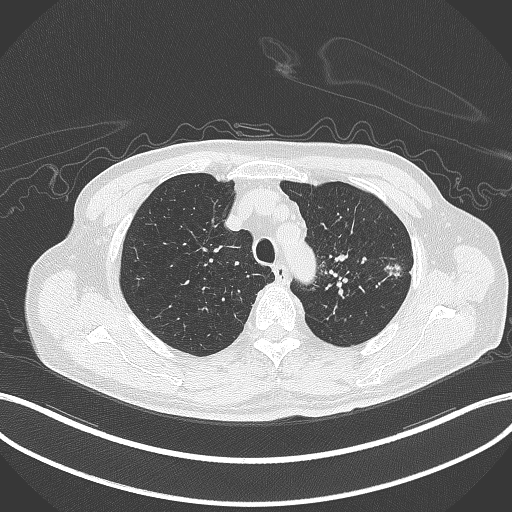
Chest CT, one axial slice; position 350 of 417 along the scan axis; reconstruction kernel B70f; lung window (W 1500 / L -600 HU); 1 mm slice thickness; 512 × 512 image matrix, field of view 400 × 400 mm. Male patient, age 77 years. Case-level facts recorded for this patient, not image findings: clinical TNM (as recorded): T3 N1 M0.
Annotated regions visible in this slice (bounding box drawn by a radiologist):
- lung tumour (recorded histology: adenocarcinoma): bounding box [x1, y1, x2, y2] px = [383, 263, 404, 279]